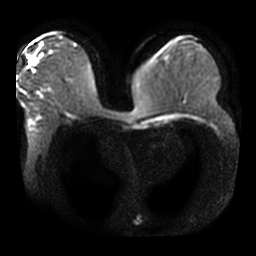
Breast MRI, one axial slice; position 16 of 42 along the scan axis; diffusion-weighted series; image 2 of 4 stored at this slice position (different b-values; order by instance number); 3 T; 5 mm slice thickness; 256 × 256 image matrix. Female patient.
Annotated regions visible in this slice (outlined manually by an expert reader):
- tumour on diffusion-weighted imaging: bounding box (x1, y1, x2, y2) in pixels: (34, 59, 37, 65)